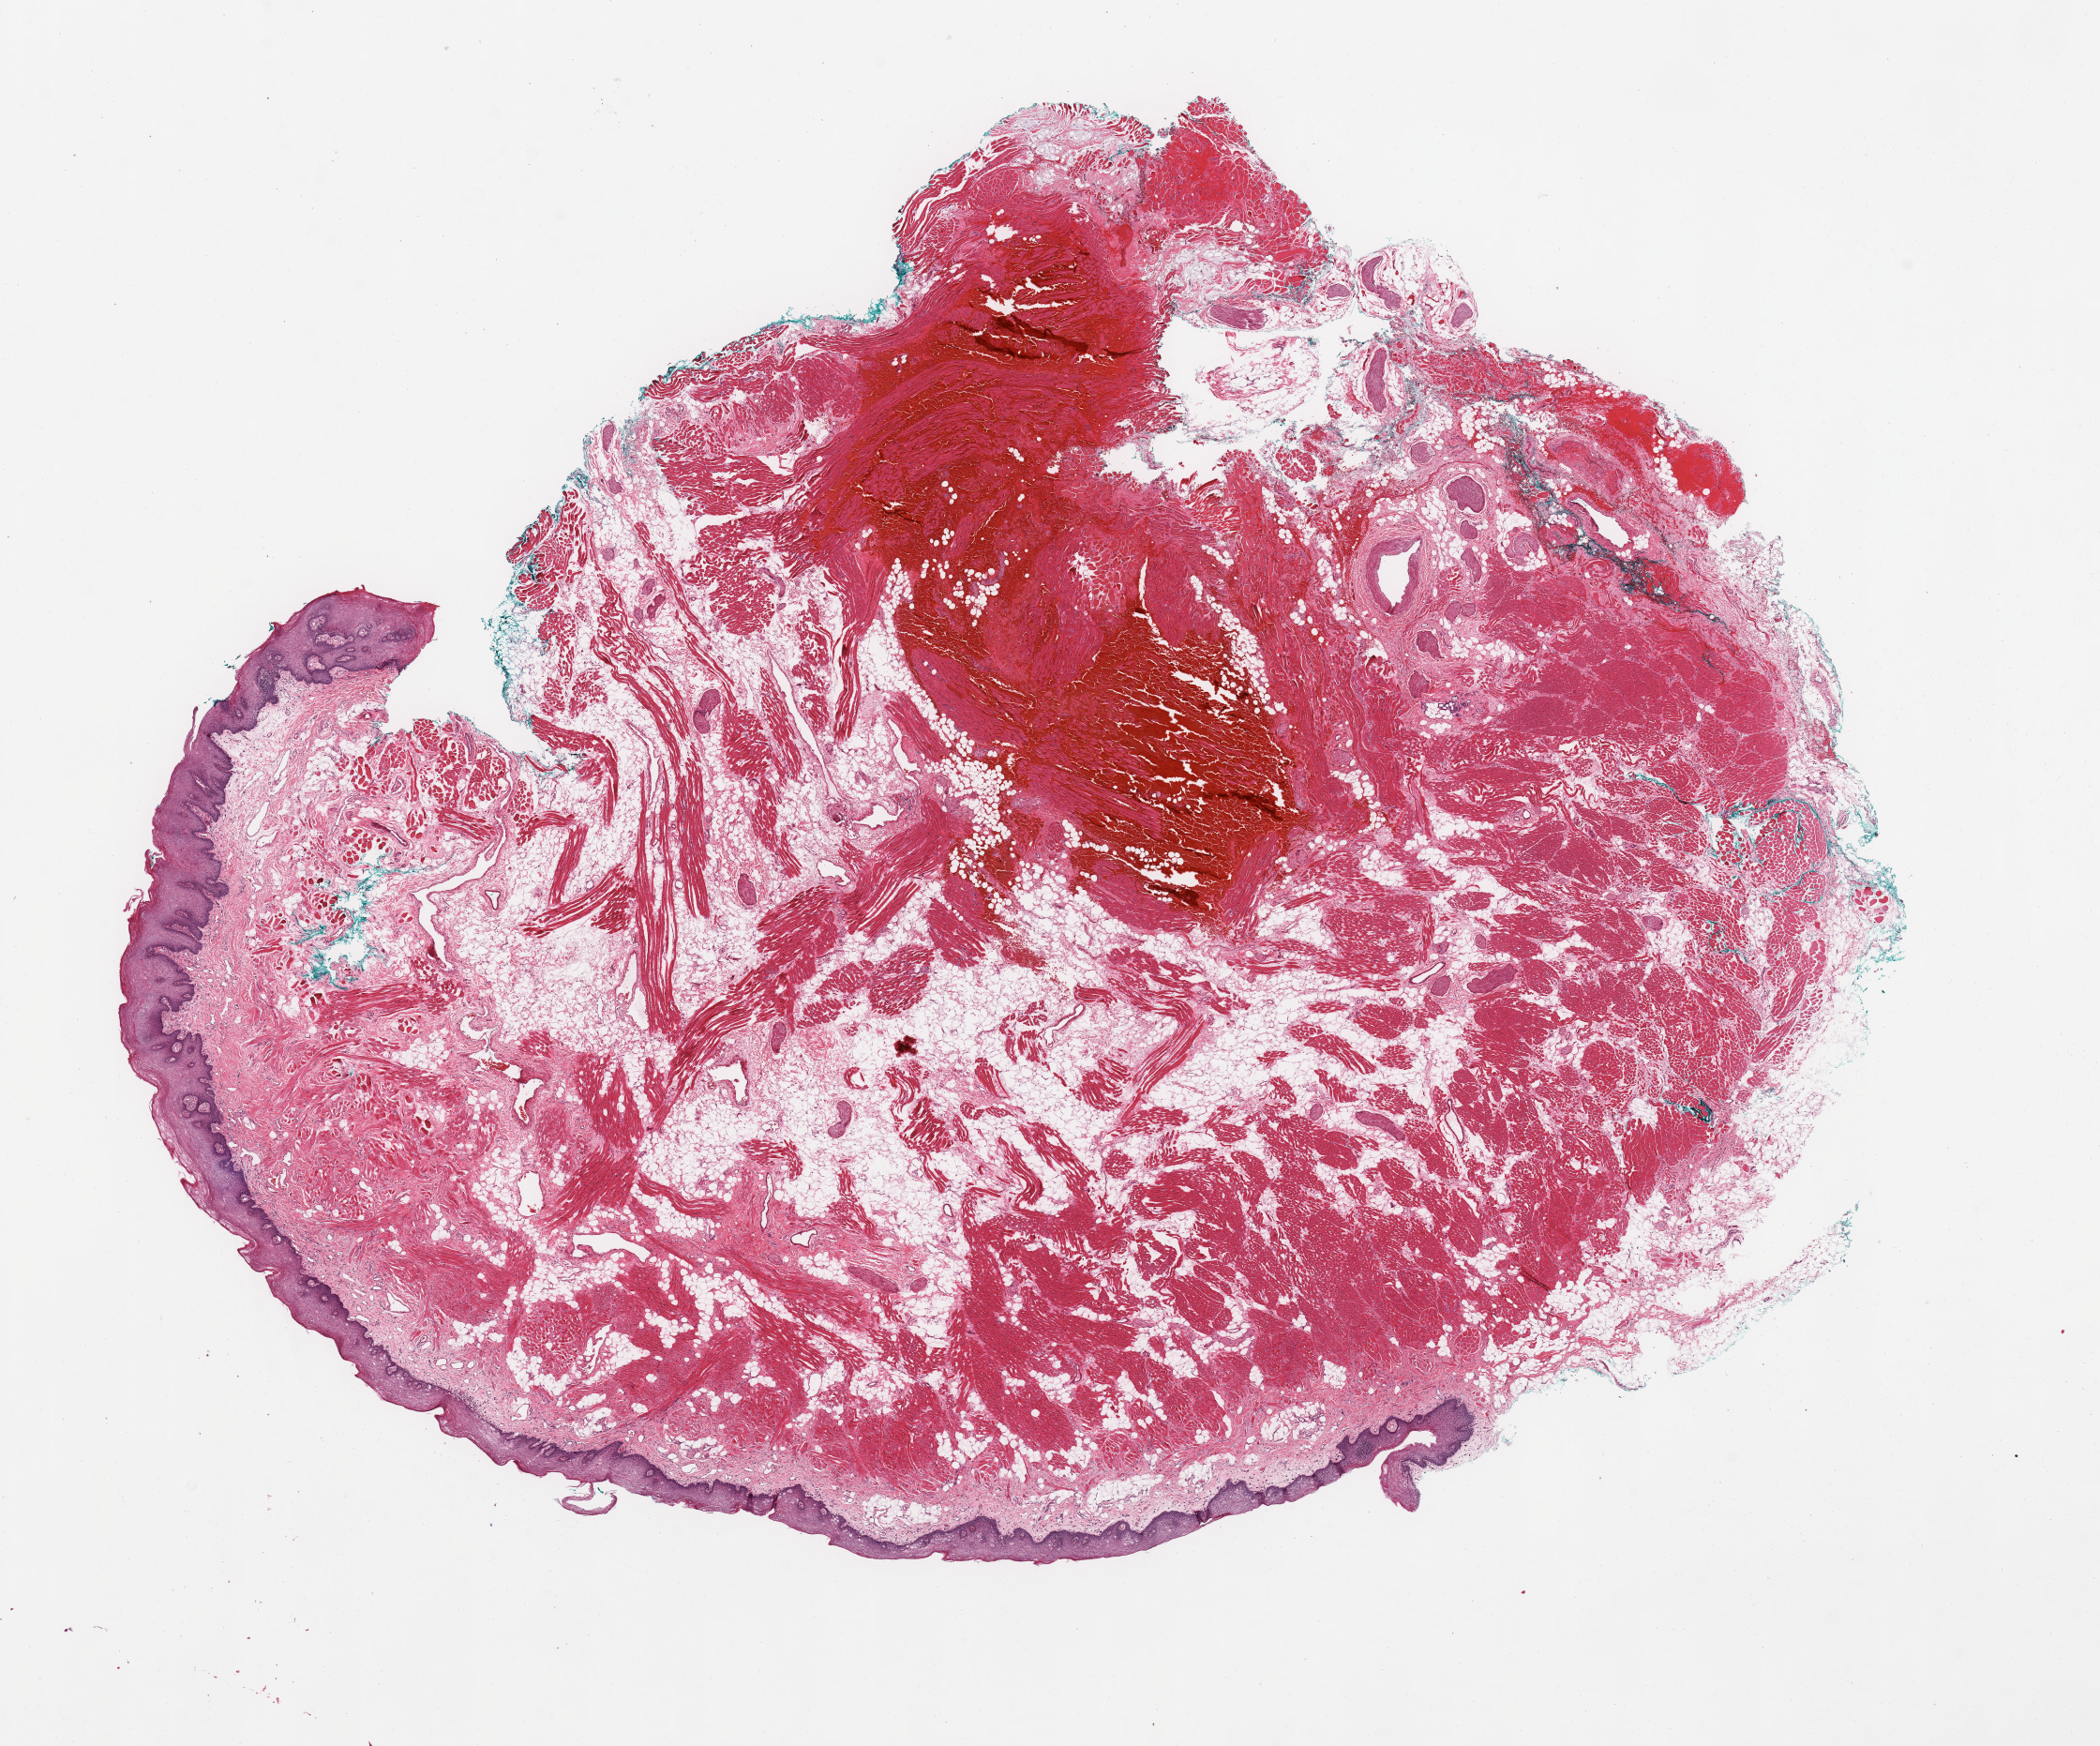
Whole-slide histology image, H&E-stained — shown as a low-resolution overview of the whole scanned area (about 17.7 x 14.7 mm, from a 20x scan). Head and neck, normal (non-tumour) tissue. Male, 50 y/o.
* this section: normal (non-tumour) tissue from the same patient
* patient diagnosis: Squamous cell carcinoma, NOS (tongue, NOS)